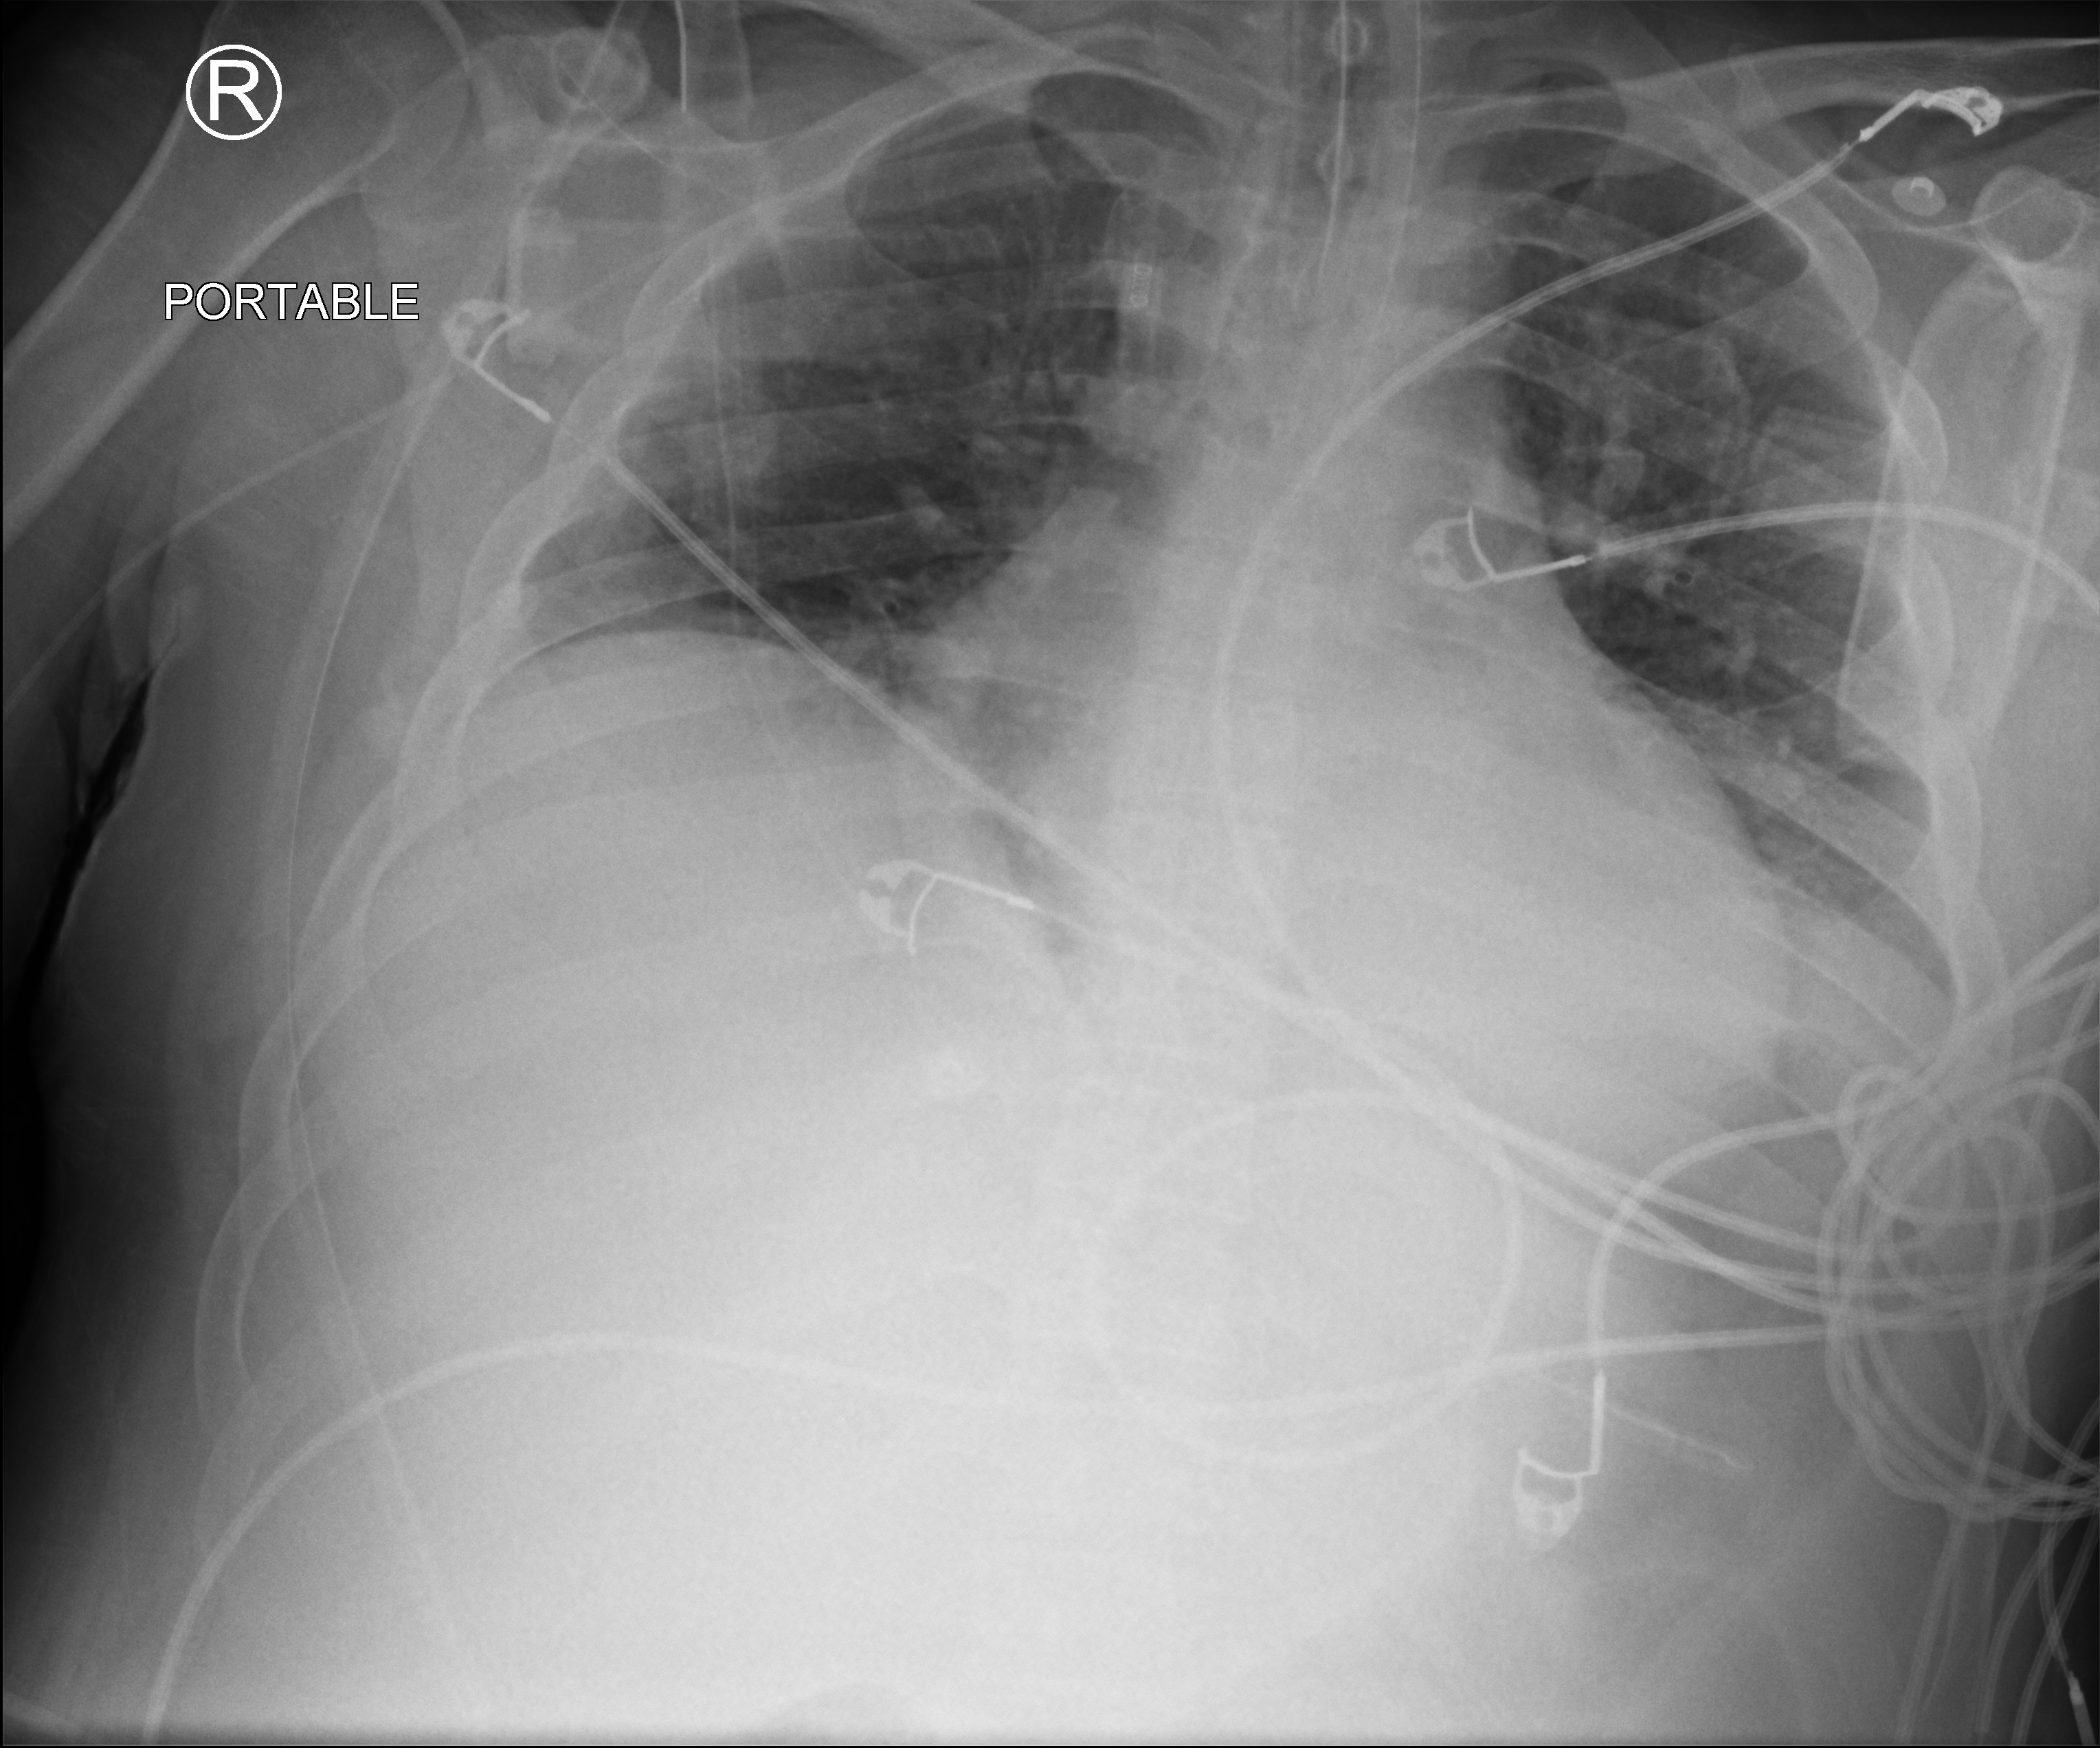
Chest X-ray (portable); anteroposterior (AP) projection. Male patient hospitalised with COVID-19, age 18–59 years.
Admission-level facts for this patient (not findings on this image; timing relative to this image not recorded): admitted to intensive care during this hospital stay: yes; chronic kidney disease (admission record): no.